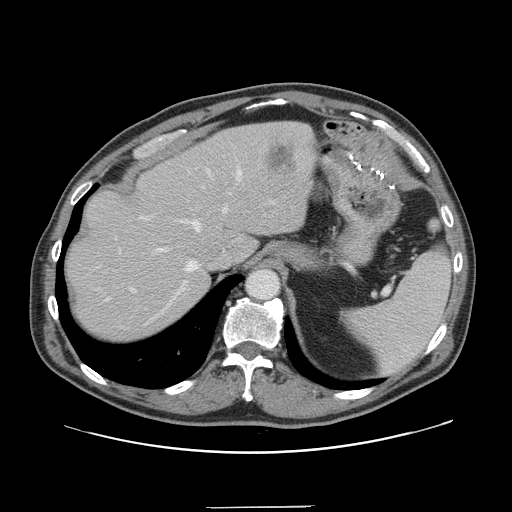
Contrast-enhanced abdominal CT, one axial slice. Slice 114 of 139 in the series (ordered by position). 120 kVp. Soft-tissue window (W 400 / L 40 HU). 2.5 mm slice thickness. 512 × 512 image matrix, field of view 397 × 397 mm. Male patient, age 64 years. From the clinical record (not read from this slice): diagnosis: colorectal cancer liver metastases, imaged before liver resection; multiple liver metastases: yes; largest metastasis: 3.5 cm; disease in both lobes: yes.
Annotated regions visible in this slice (outlined manually by an expert reader):
- hepatic veins: bounding box <158,170,242,291> (left, top, right, bottom; pixels)
- liver: <65,122,317,340>
- planned liver remnant (the part of the liver to remain after resection): <66,125,268,340>
- portal vein (with intrahepatic branches): <130,187,204,292>
- liver metastasis: <267,146,296,175>